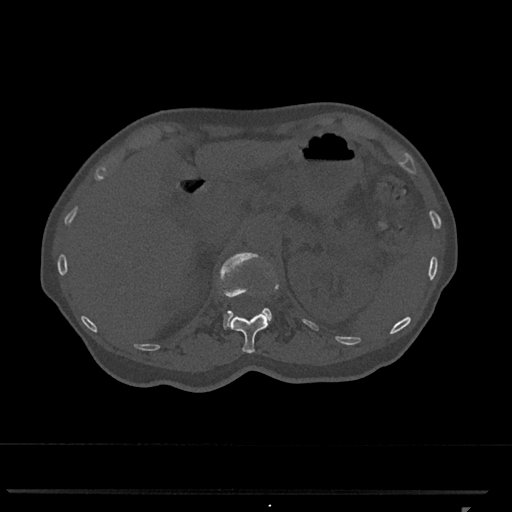
CT including the spine, one axial slice; slice 439 of 793 in the series (ordered by position); reconstruction kernel Br40s/3; 120 kVp; bone window (W 1800 / L 400 HU); 0.5 mm slice thickness; 512 × 512 image matrix, field of view 380 × 380 mm. Female patient, age 62 years. Case-level facts recorded for this patient, not image findings: primary cancer: renal.
Outlined on this slice (semi-automatically segmented with operator editing):
- L1 vertebra: box from (x=219, y=252) to (x=272, y=329) px
- T12 vertebra: (x=228, y=253)–(x=279, y=353)